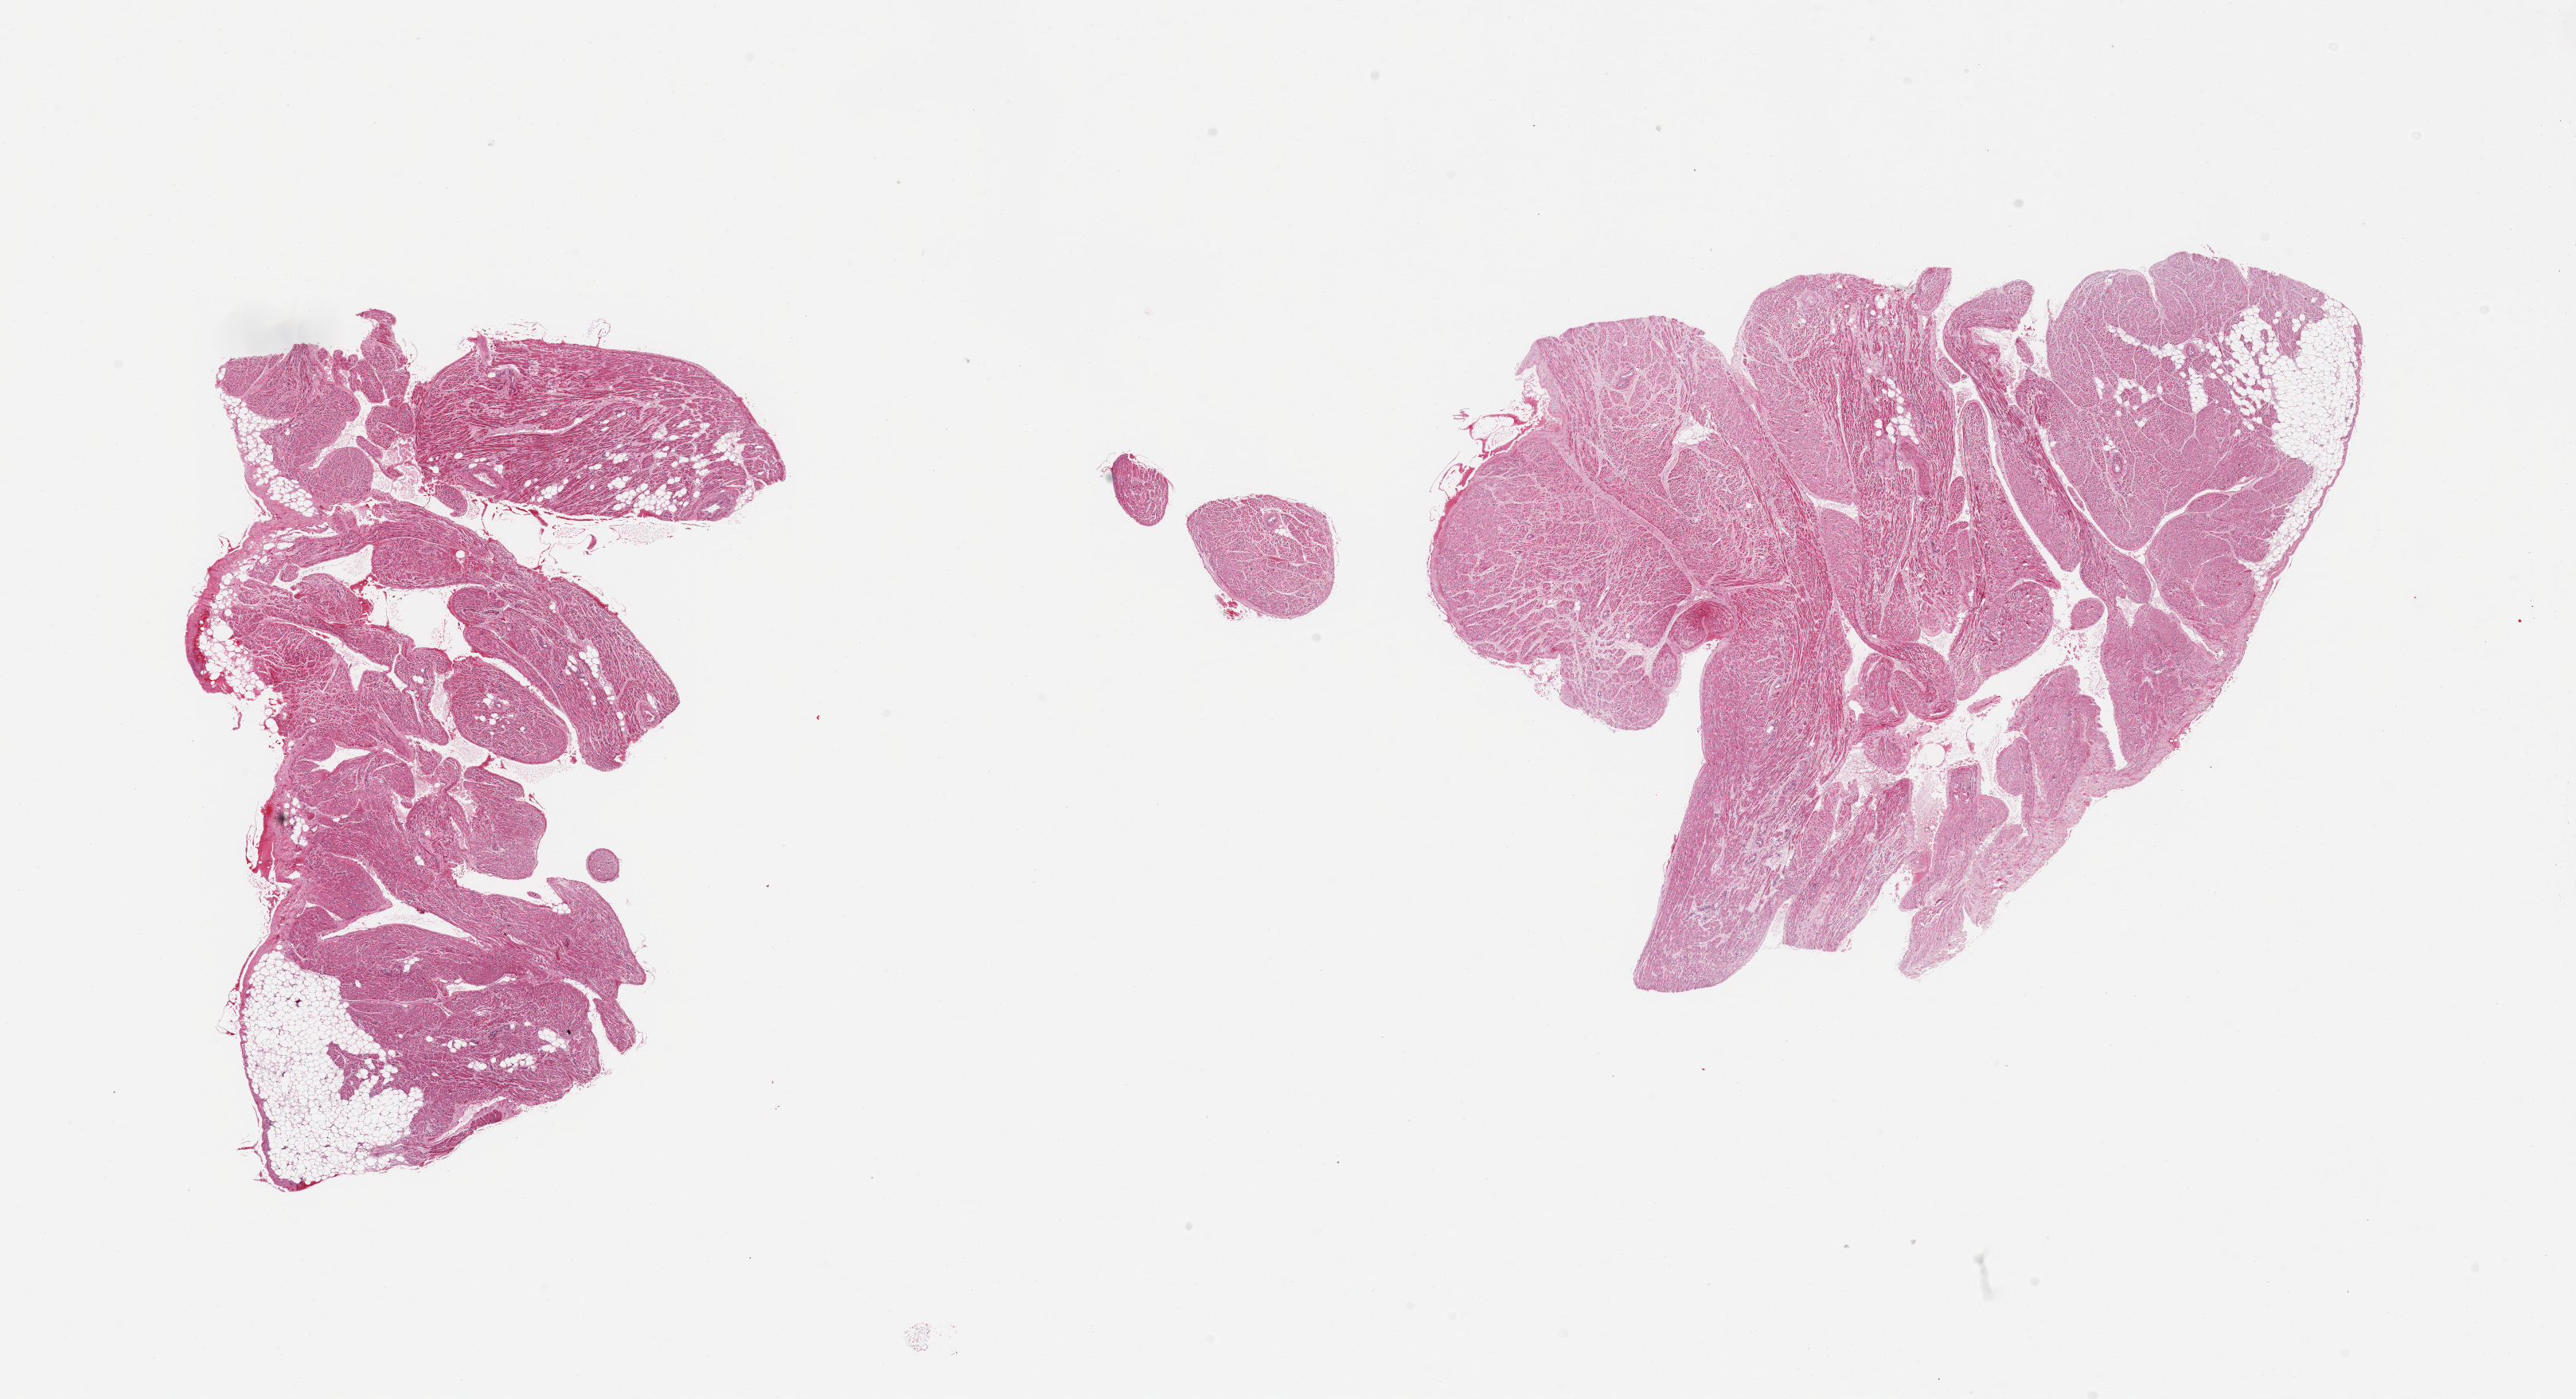
Whole-slide image, hematoxylin and eosin (H&E) stain, brightfield, a low-resolution overview of the entire scanned area, about 25.6 x 13.9 mm (acquisition: 20x scan). PAXgene-fixed paraffin-embedded (PFPE) section. Sampled site (target tissue): auricular appendage. Donor tissue sample.
Pathologist's review note for this sample: 2 pieces, no abnormalities.